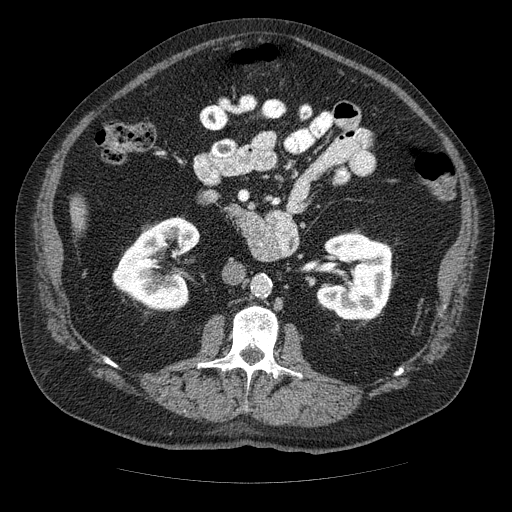
Contrast-enhanced abdominal CT (liver protocol), one axial slice; 120 kVp; soft-tissue window (W 400 / L 40 HU); 512 × 512 image matrix. Case-level facts recorded for this patient, not image findings: diagnosis: hepatocellular carcinoma (patient treated with transarterial chemoembolisation; whether this scan precedes or follows treatment is not stated here); TNM stage (as recorded): Stage-IIIA; Child-Pugh class: A; tumour nodularity: multinodular.
Structures marked on this image (semi-automatic segmentation, software-assisted and operator-edited):
- liver parenchyma outside the tumour (the mass and vessels are separate outlines, so this box may not span the whole liver): bounding box <70,200,86,230> (left, top, right, bottom; pixels)